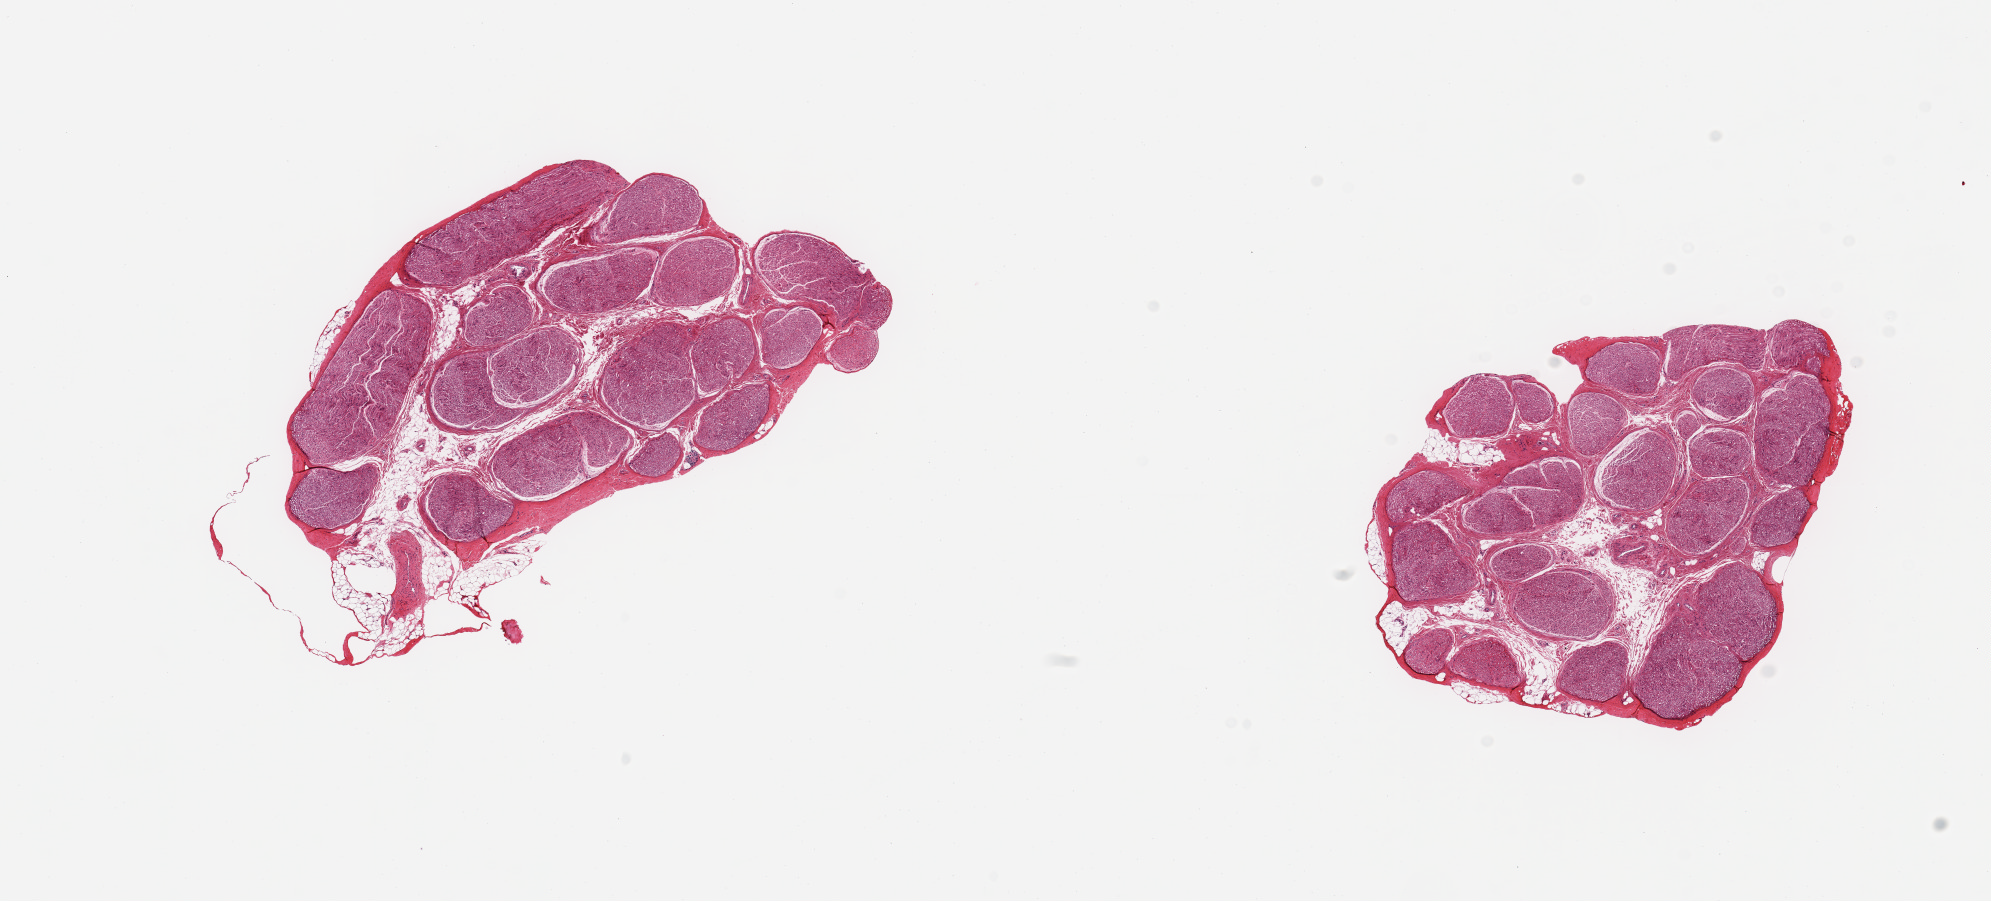
Whole-slide image, H&E stain, brightfield, low-resolution overview of the scanned area, about 15.8 x 7.1 mm, PAXgene-fixed, paraffin-embedded tissue, sampled site (target tissue): tibial nerve, tissue donor sample. Female donor.
- reviewer comment on this tissue sample: 2 pieces; includes ~10-15% internal and attached fat